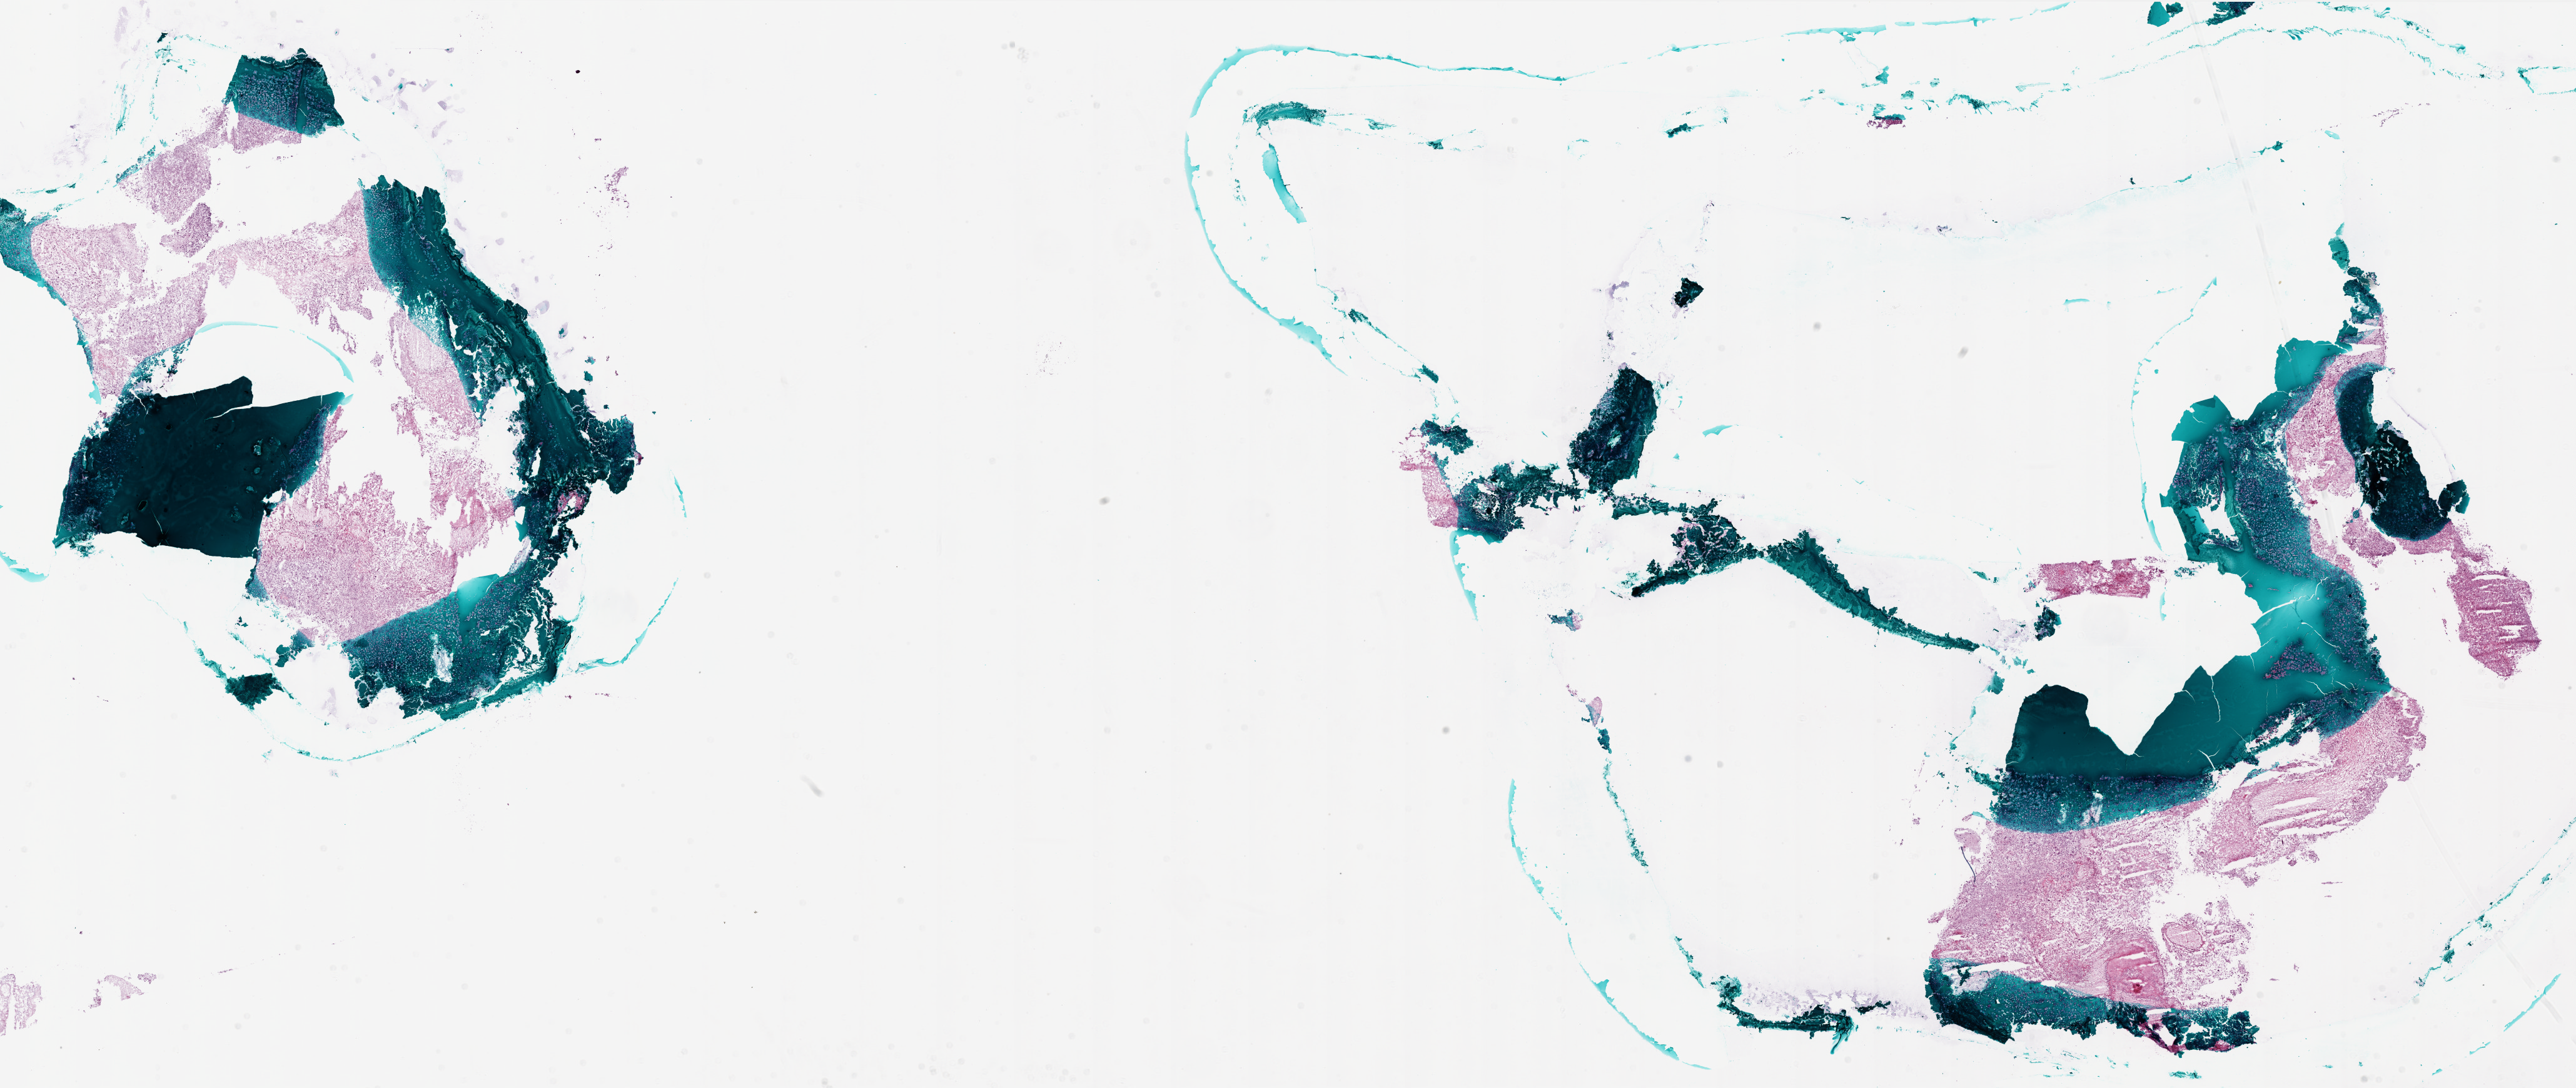
Hematoxylin and eosin (H&E) stained whole-slide image, shown as a low-resolution overview of the whole scanned area (about 33.0 x 13.9 mm, acquisition: 20x scan), frozen section from the bottom of the tissue portion, brain, primary tumour sample. Female, age 68 years at initial diagnosis. Pathologist review of this section (percent, as recorded): tumour cells 75%, tumour nuclei 100%, normal cells 0%, stromal cells 0%, necrosis 25%.
• diagnosis: Glioblastoma